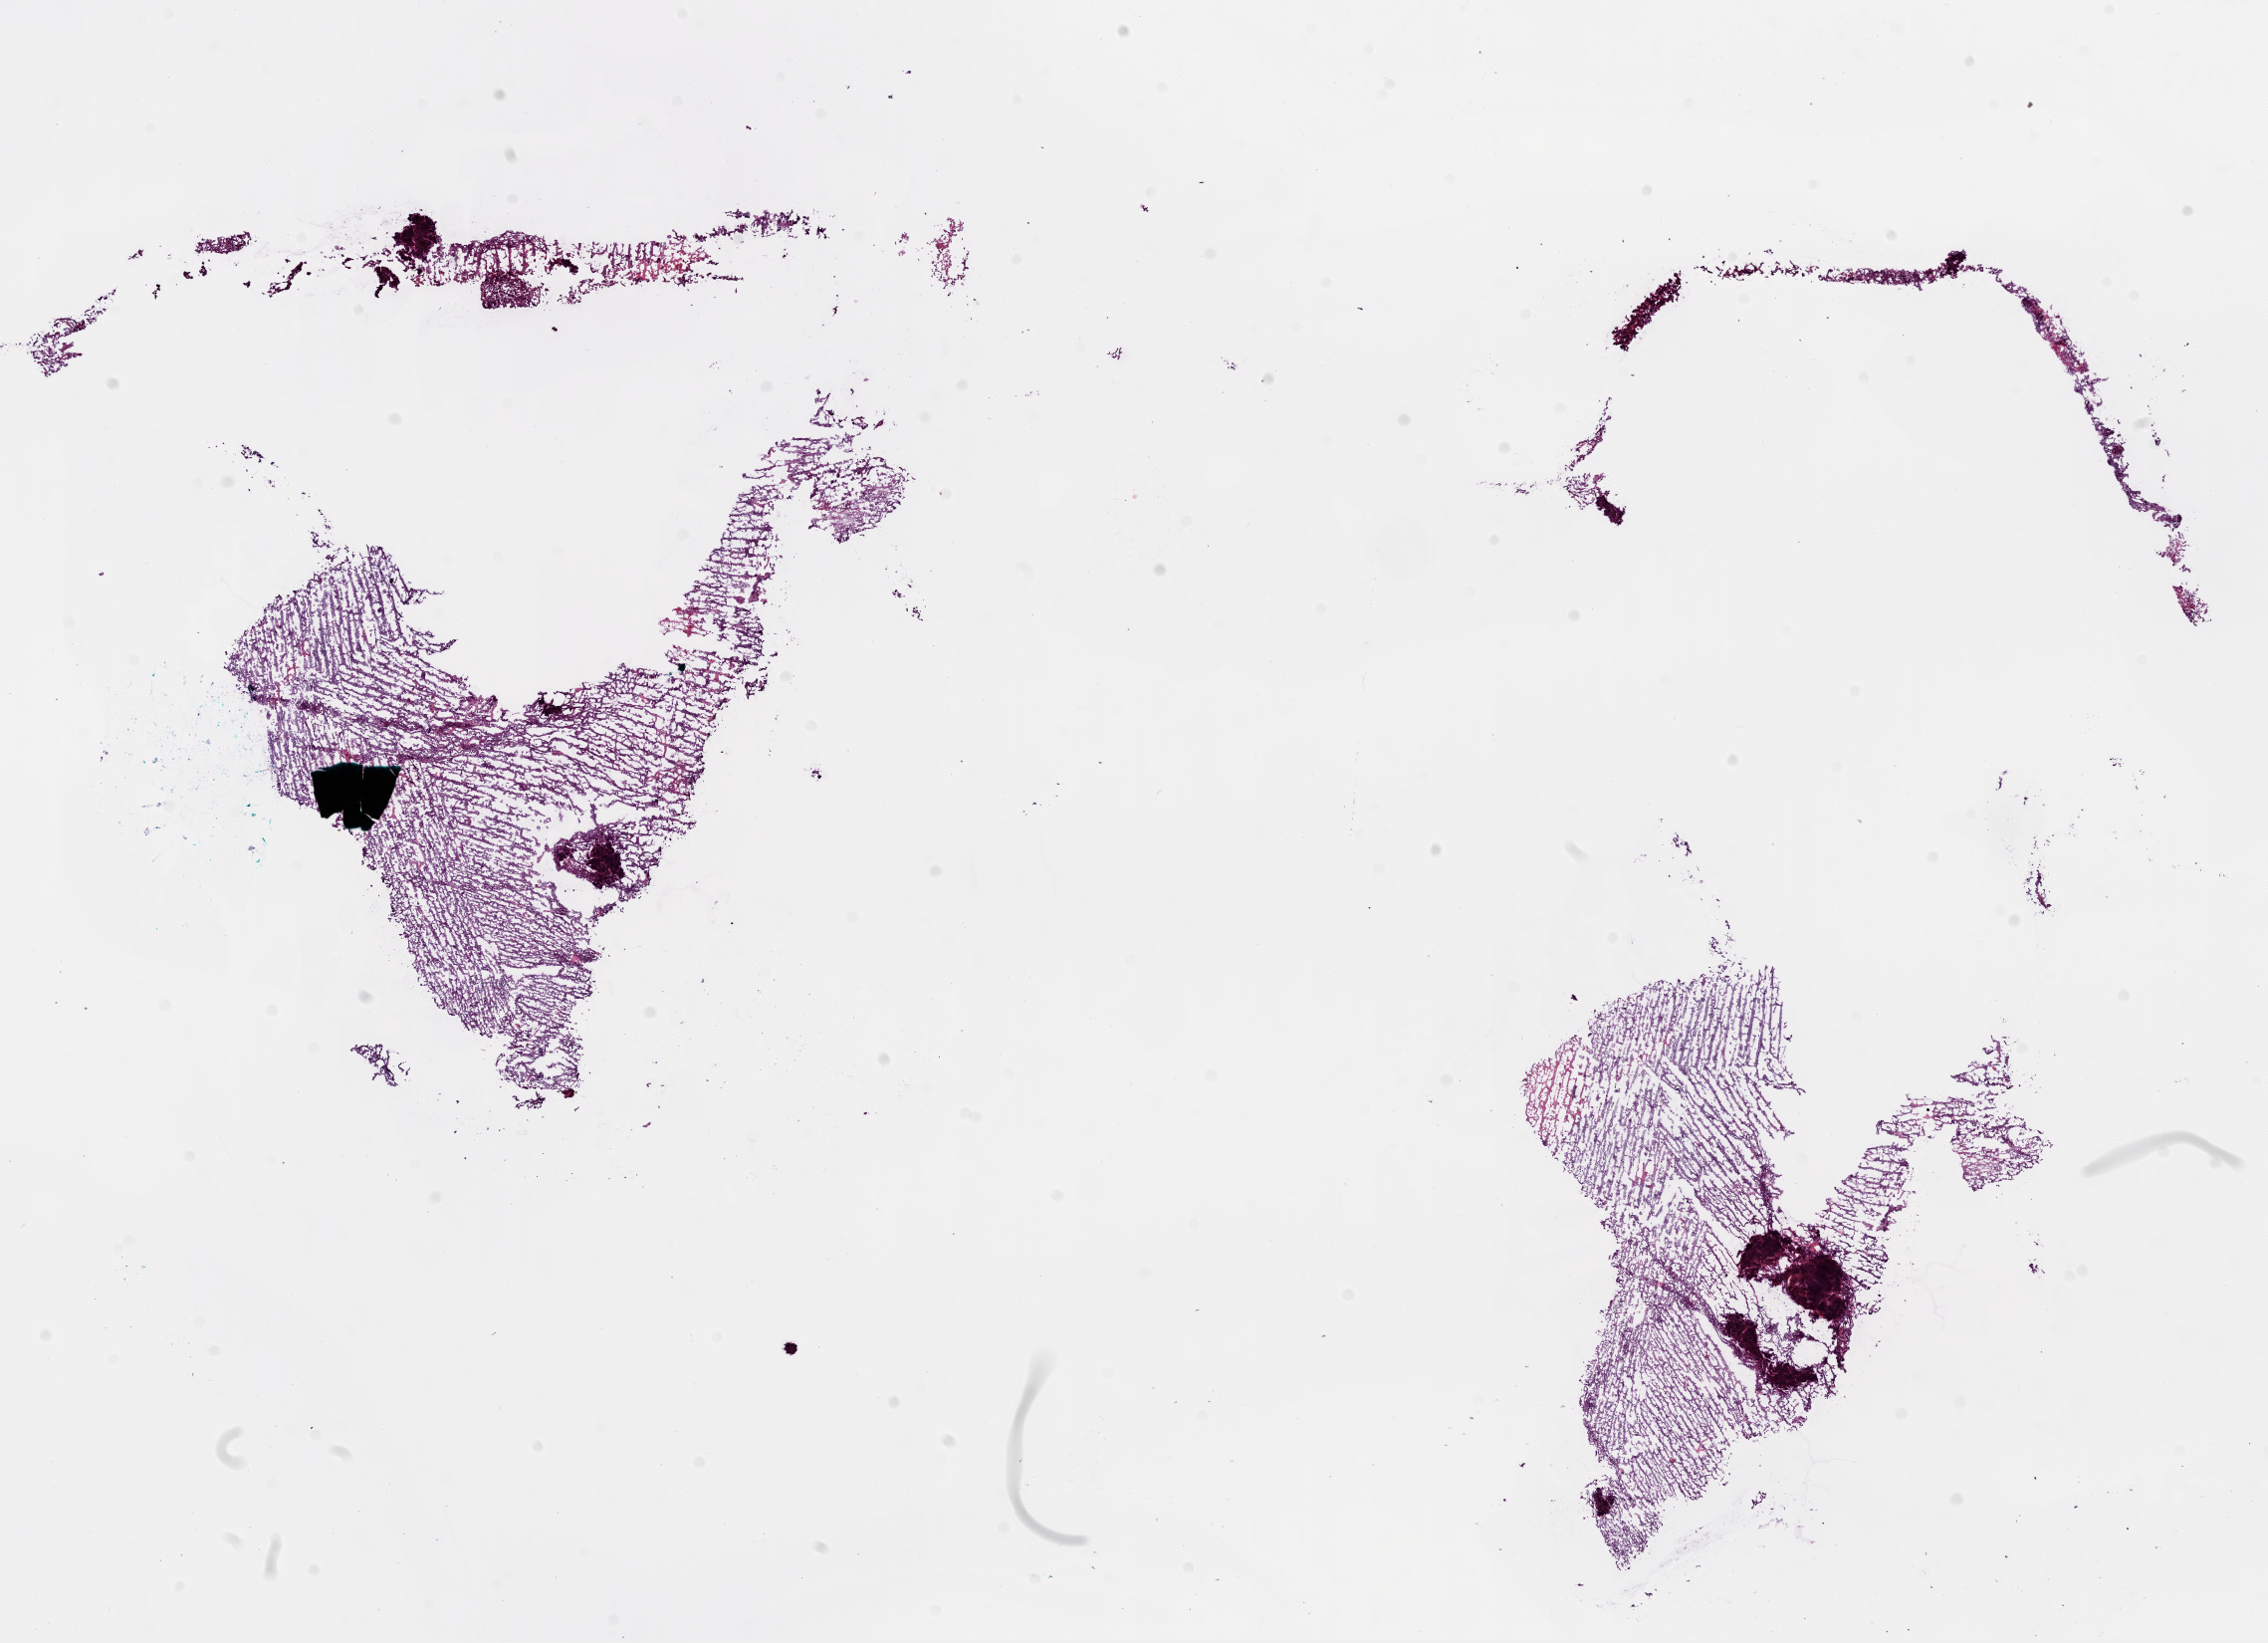
H&E-stained whole-slide image — low-resolution overview of the scanned area, about 18.4 x 13.3 mm; frozen section from the bottom of the tissue portion; brain, primary tumour sample. Male, age 58 years at initial diagnosis. Composition of this section per pathologist review: tumour cells 90%, tumour nuclei 90%, normal cells 0%, stromal cells 10%, necrosis 0%.
• diagnosis: Glioblastoma